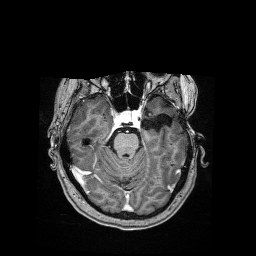
Brain MRI from a brain-tumour surgery series, one axial slice; T1-weighted post-contrast; 256 × 256 image matrix, field of view 256 × 256 mm. From the clinical record (not read from this slice): histopathology: Dysembryoplastic neuroepithelial tumor; WHO grade: 1; IDH mutation: no; tumour location: Left Temporal.
Outlined on this slice (expert manual segmentation):
- tumour: bounding box (x1, y1, x2, y2) in pixels: (148, 113, 152, 117)